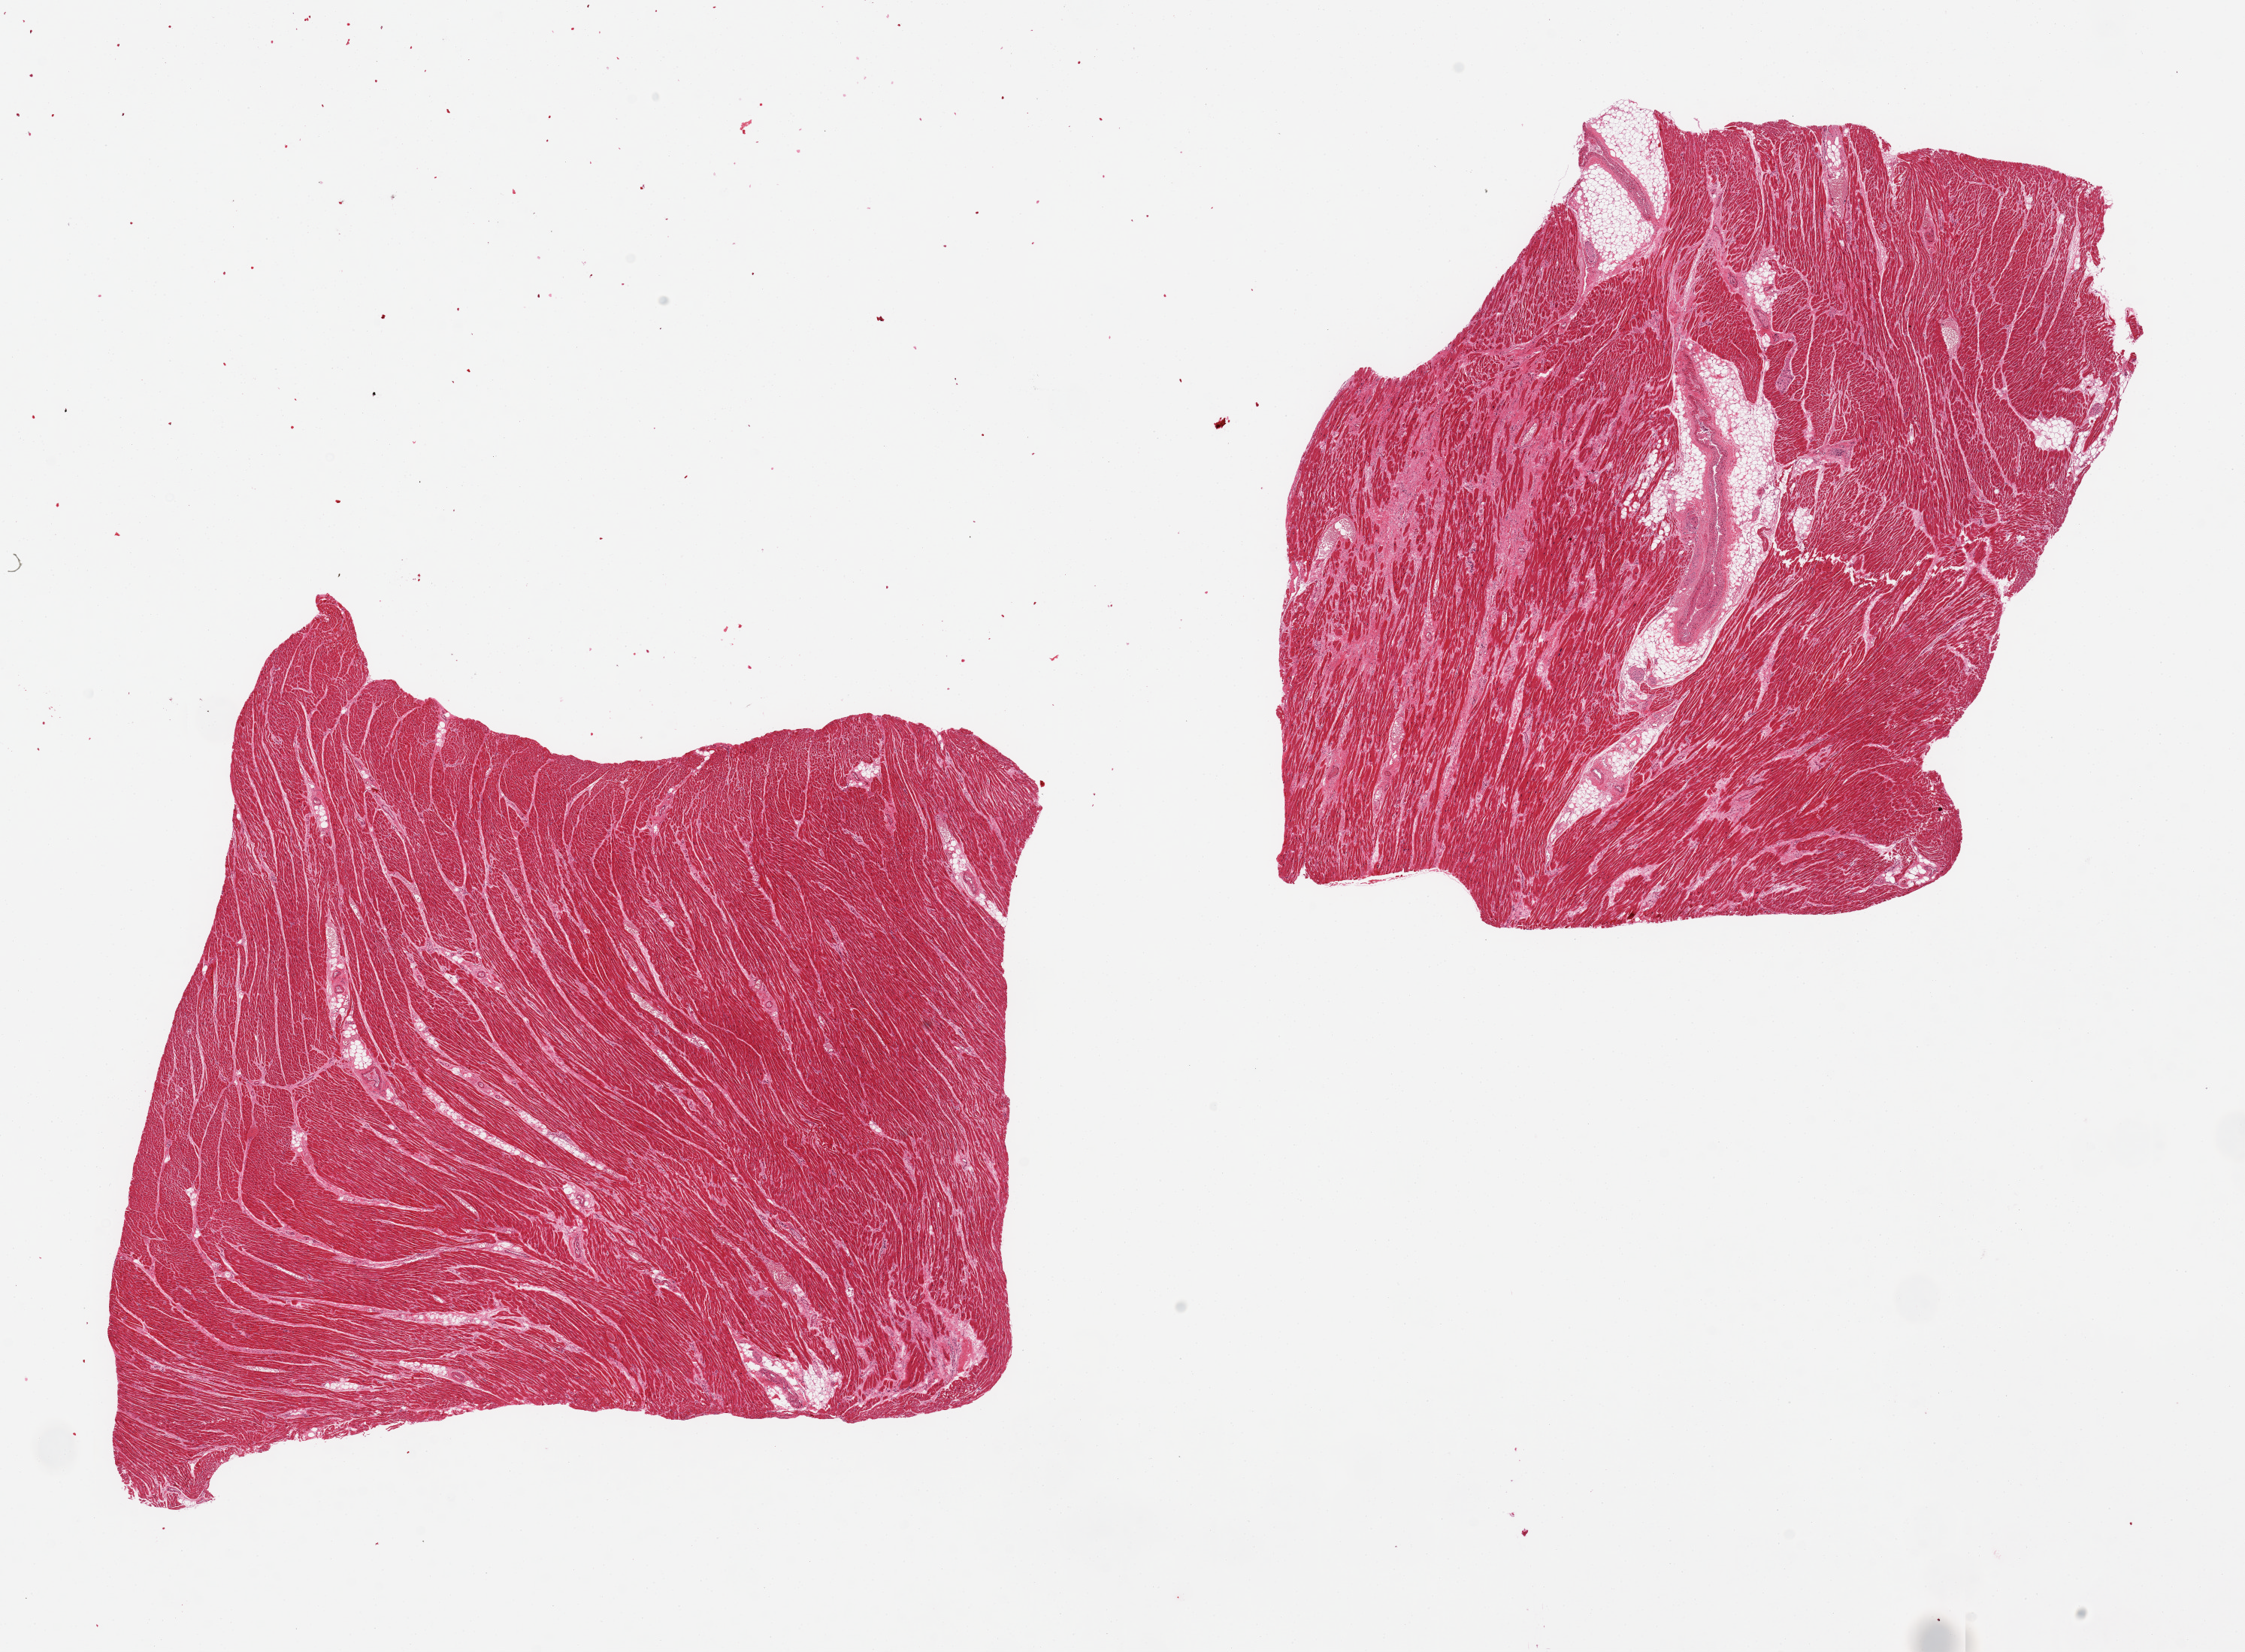
Whole-slide image, haematoxylin and eosin stain, a low-resolution overview of the entire scanned area, about 23.6 x 17.4 mm; PAXgene-fixed paraffin-embedded (PFPE) section; sampled site (target tissue): heart; tissue donor sample. Male donor.
Review note (as recorded): 2 pieces; 1 has patchy fibrous scars <10% & internal fat 10%.